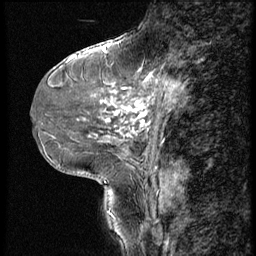
Breast MRI (dynamic contrast-enhanced), one sagittal slice. 3 images stored at this slice position (order not interpretable as contrast timing). 1.5 T. TE 4.2 ms, TR 9 ms. 2.5 mm slice thickness. 256 × 256 image matrix, field of view 180 × 180 mm. Patient: female, 46 years. From the clinical record (not read from this slice): setting: breast cancer imaged before/during neoadjuvant chemotherapy; receptor status: HER2-positive.
Annotated regions visible in this slice (semi-automatic segmentation, software-assisted and operator-edited):
- analysis volume of interest (the breast-tissue region the enhancement analysis was run in; not a lesion): bounding box <79,68,190,143> (left, top, right, bottom; pixels)
- tumour enhancement mask (voxels above the 140 % enhancement threshold inside the analysis volume of interest): <105,77,175,136>